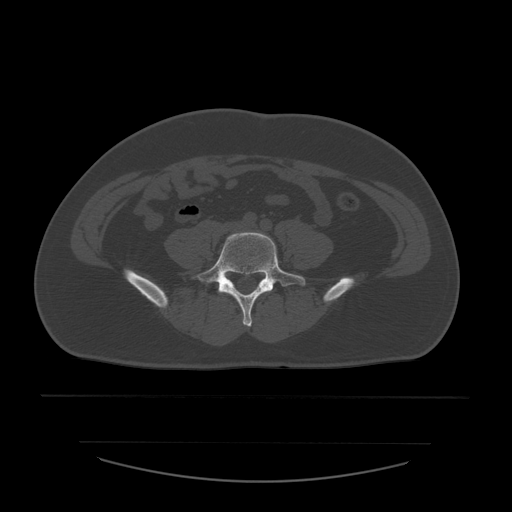
CT including the spine, one axial slice; slice 123 of 532 in the series (ordered by position); reconstruction kernel STANDARD; 120 kVp; bone window (W 1800 / L 400 HU); 1.25 mm slice thickness; 512 × 512 image matrix, field of view 441 × 441 mm. Patient age 44 years. Case-level facts recorded for this patient, not image findings: primary cancer: soft tissue sarcoma.
Structures marked on this image (semi-automatic segmentation, software-assisted and operator-edited):
- L5 vertebra: bounding box (x1, y1, x2, y2) in pixels: (193, 233, 306, 327)